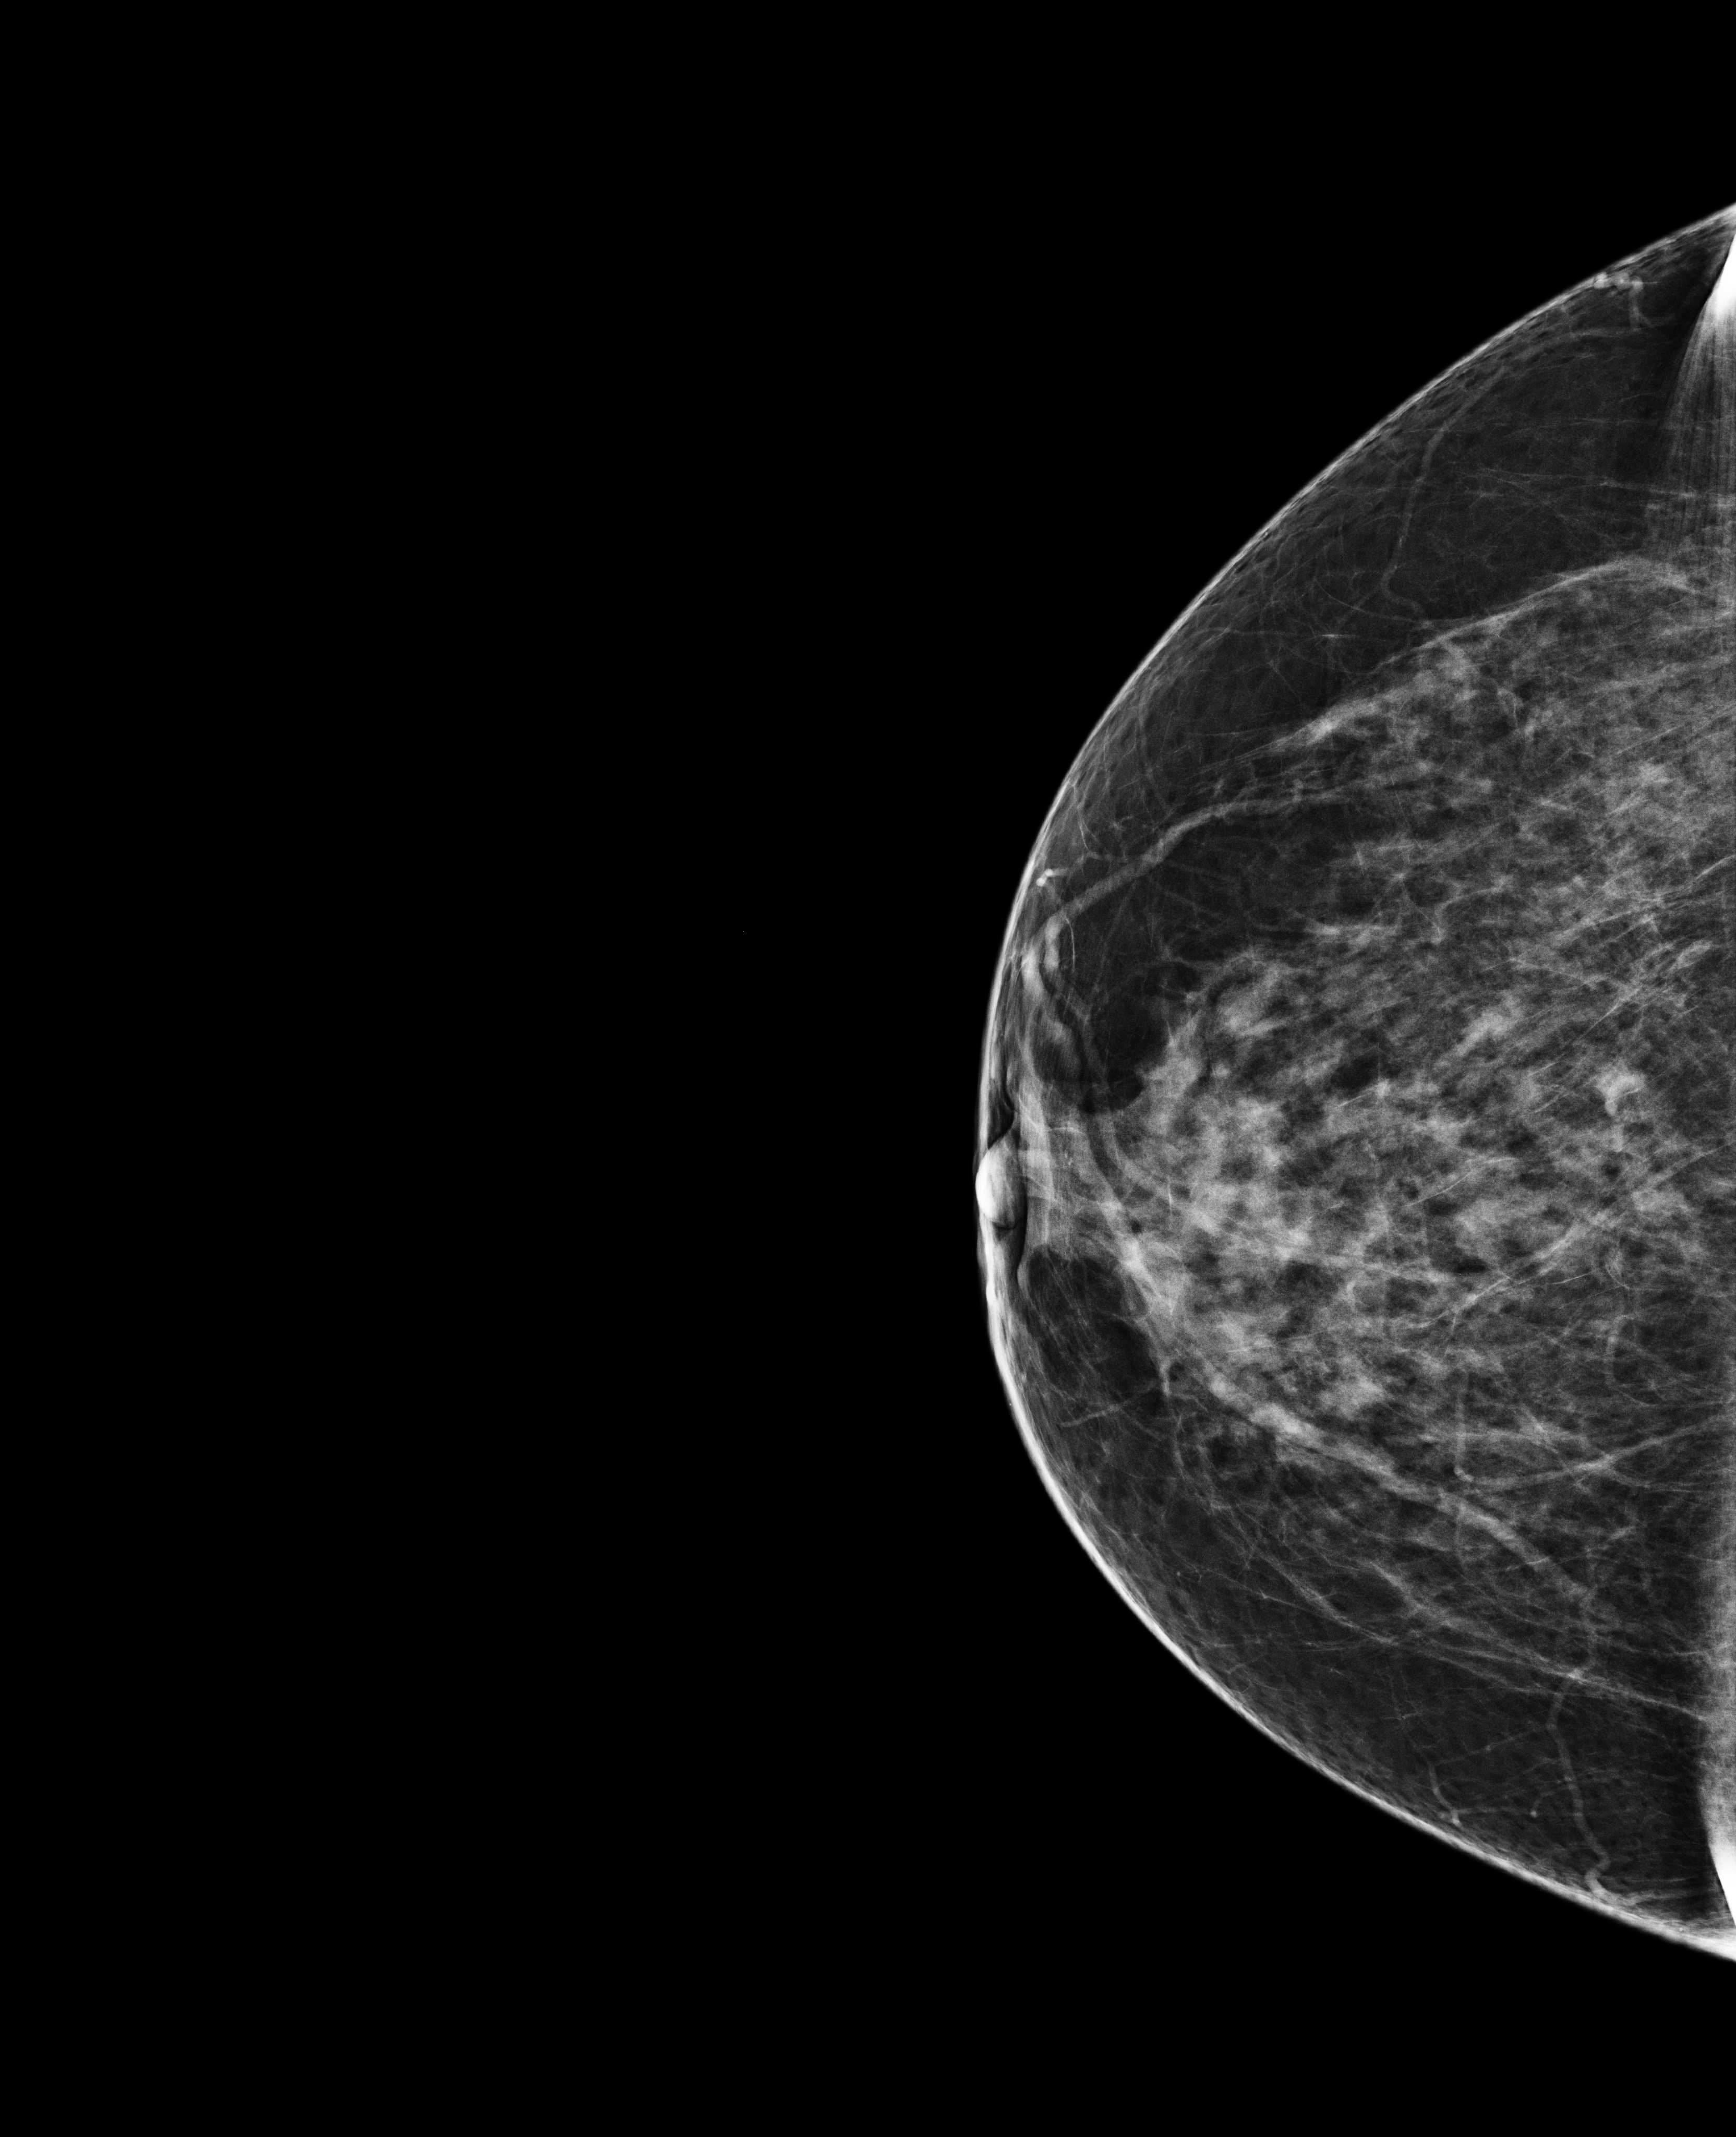
Digital mammogram (FFDM); right breast; CC view; annual screening mammography examination; system: Selenia Dimensions. Patient aged 71 years (female).
- breast density at the screening exam (both breasts): heterogeneously dense (BI-RADS density category c)
- final BI-RADS assessment for this screening round (tomosynthesis exam, both breasts): category 2
- recall: no recall after this screen